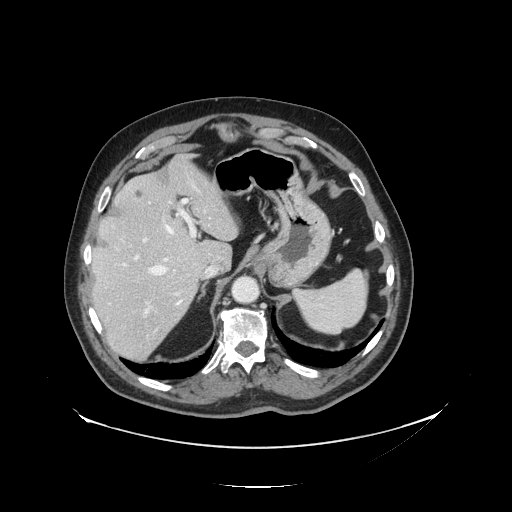
Contrast-enhanced abdominal CT, one axial slice. Slice 100 of 138 in the series (ordered by position). Reconstruction kernel STANDARD. Intravenous contrast given. Soft-tissue window (W 400 / L 40 HU). 2.5 mm slice thickness. 512 × 512 image matrix. Male patient, age 77 years. From the clinical record (not read from this slice): diagnosis: colorectal cancer liver metastases, imaged before liver resection; multiple liver metastases: no; largest metastasis: 1.5 cm; chemotherapy before resection: no.
Structures marked on this image (outlined manually by an expert reader):
- hepatic veins: bounding box <148,217,211,306> (left, top, right, bottom; pixels)
- liver: <92,158,237,360>
- planned liver remnant (the part of the liver to remain after resection): <92,158,237,288>
- portal vein (with intrahepatic branches): <134,199,210,317>
- liver metastasis: <170,210,178,219>
- liver metastasis: <136,191,143,198>